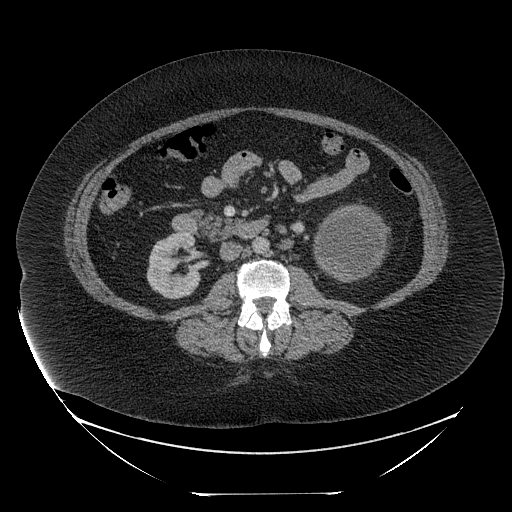
Contrast-enhanced abdominal CT, one axial slice. Slice 114 of 205 in the series (ordered by position). Intravenous contrast given. Soft-tissue window (W 400 / L 40 HU). 512 × 512 image matrix. Patient: female, 53 years. From the clinical record (not read from this slice): diagnosis: adrenocortical carcinoma; tumour side: left adrenal; tumour size at pathology: 17 cm; Ki-67 index: 20 %; stage (as recorded): 3.
Annotated regions visible in this slice (semi-automatically segmented with operator editing):
- mass: box from (x=317, y=207) to (x=385, y=279) px